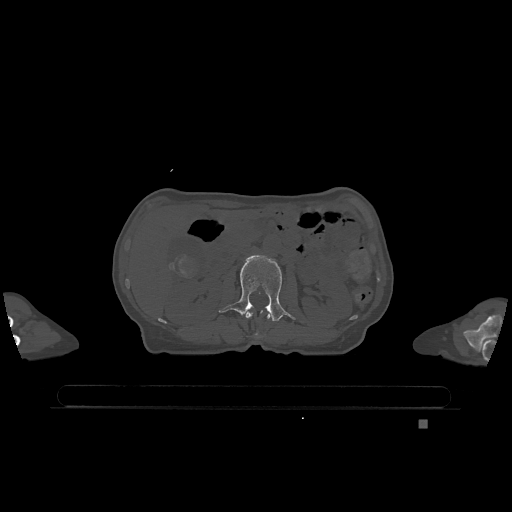
CT including the spine, one axial slice. Position 425 of 1317 along the scan axis. Bone window (W 1800 / L 400 HU). 0.5 mm slice thickness. 512 × 512 image matrix. Female patient, age 74 years. From the clinical record (not read from this slice): primary cancer: lung.
Annotated regions visible in this slice (semi-automatically segmented with operator editing):
- L1 vertebra: bounding box <243,312,270,337> (left, top, right, bottom; pixels)
- L2 vertebra: <219,255,295,321>